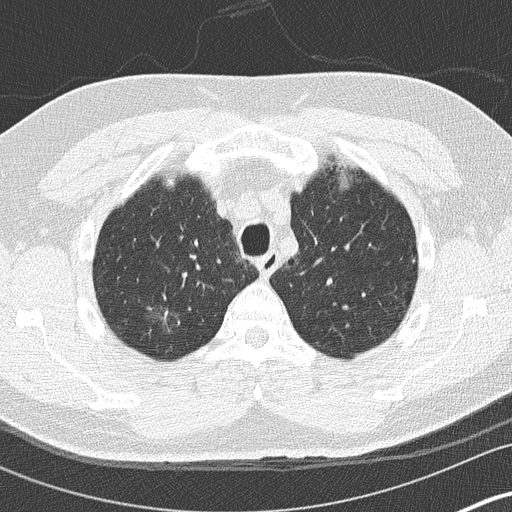
Axial slice from a low-dose chest CT screening exam. Baseline screening round. Lung window (W 1500 / L -600 HU). 2 mm slice thickness. Lung (sharp) reconstruction kernel (B50f). Slice 31 of 136 in the series. Male, age 59 years at enrolment.
Expert reader's lesion annotation, bounding box (x1, y1, x2, y2) in pixels: (142, 293, 193, 343). Screening reader's record for this exam (one nodule recorded; not confirmed to be the boxed lesion): non-calcified nodule or mass ≥4 mm, right upper lobe, 16 × 16 mm, ground glass attenuation. Official screen result: positive, change unspecified: nodule(s) >= 4 mm or enlarging nodule(s), mass(es), or other non-specific abnormalities suspicious for lung cancer. Lung cancer was diagnosed 456 days after this screen (after the second annual screen): bronchiolo-alveolar adenocarcinoma, NOS, right lower lobe, stage IA (AJCC 6th edition), 15 mm at pathology.